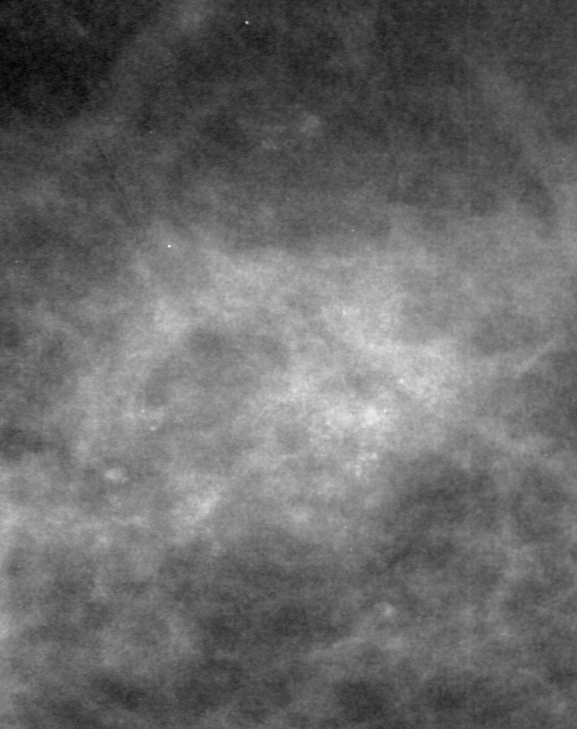
Cropped region of a digitized screen-film mammogram centred on a radiologist-marked abnormality; left breast; CC view.
Finding: calcifications, morphology amorphous, distribution clustered; BI-RADS assessment category 4; pathology result (as recorded, not read from the image): benign.